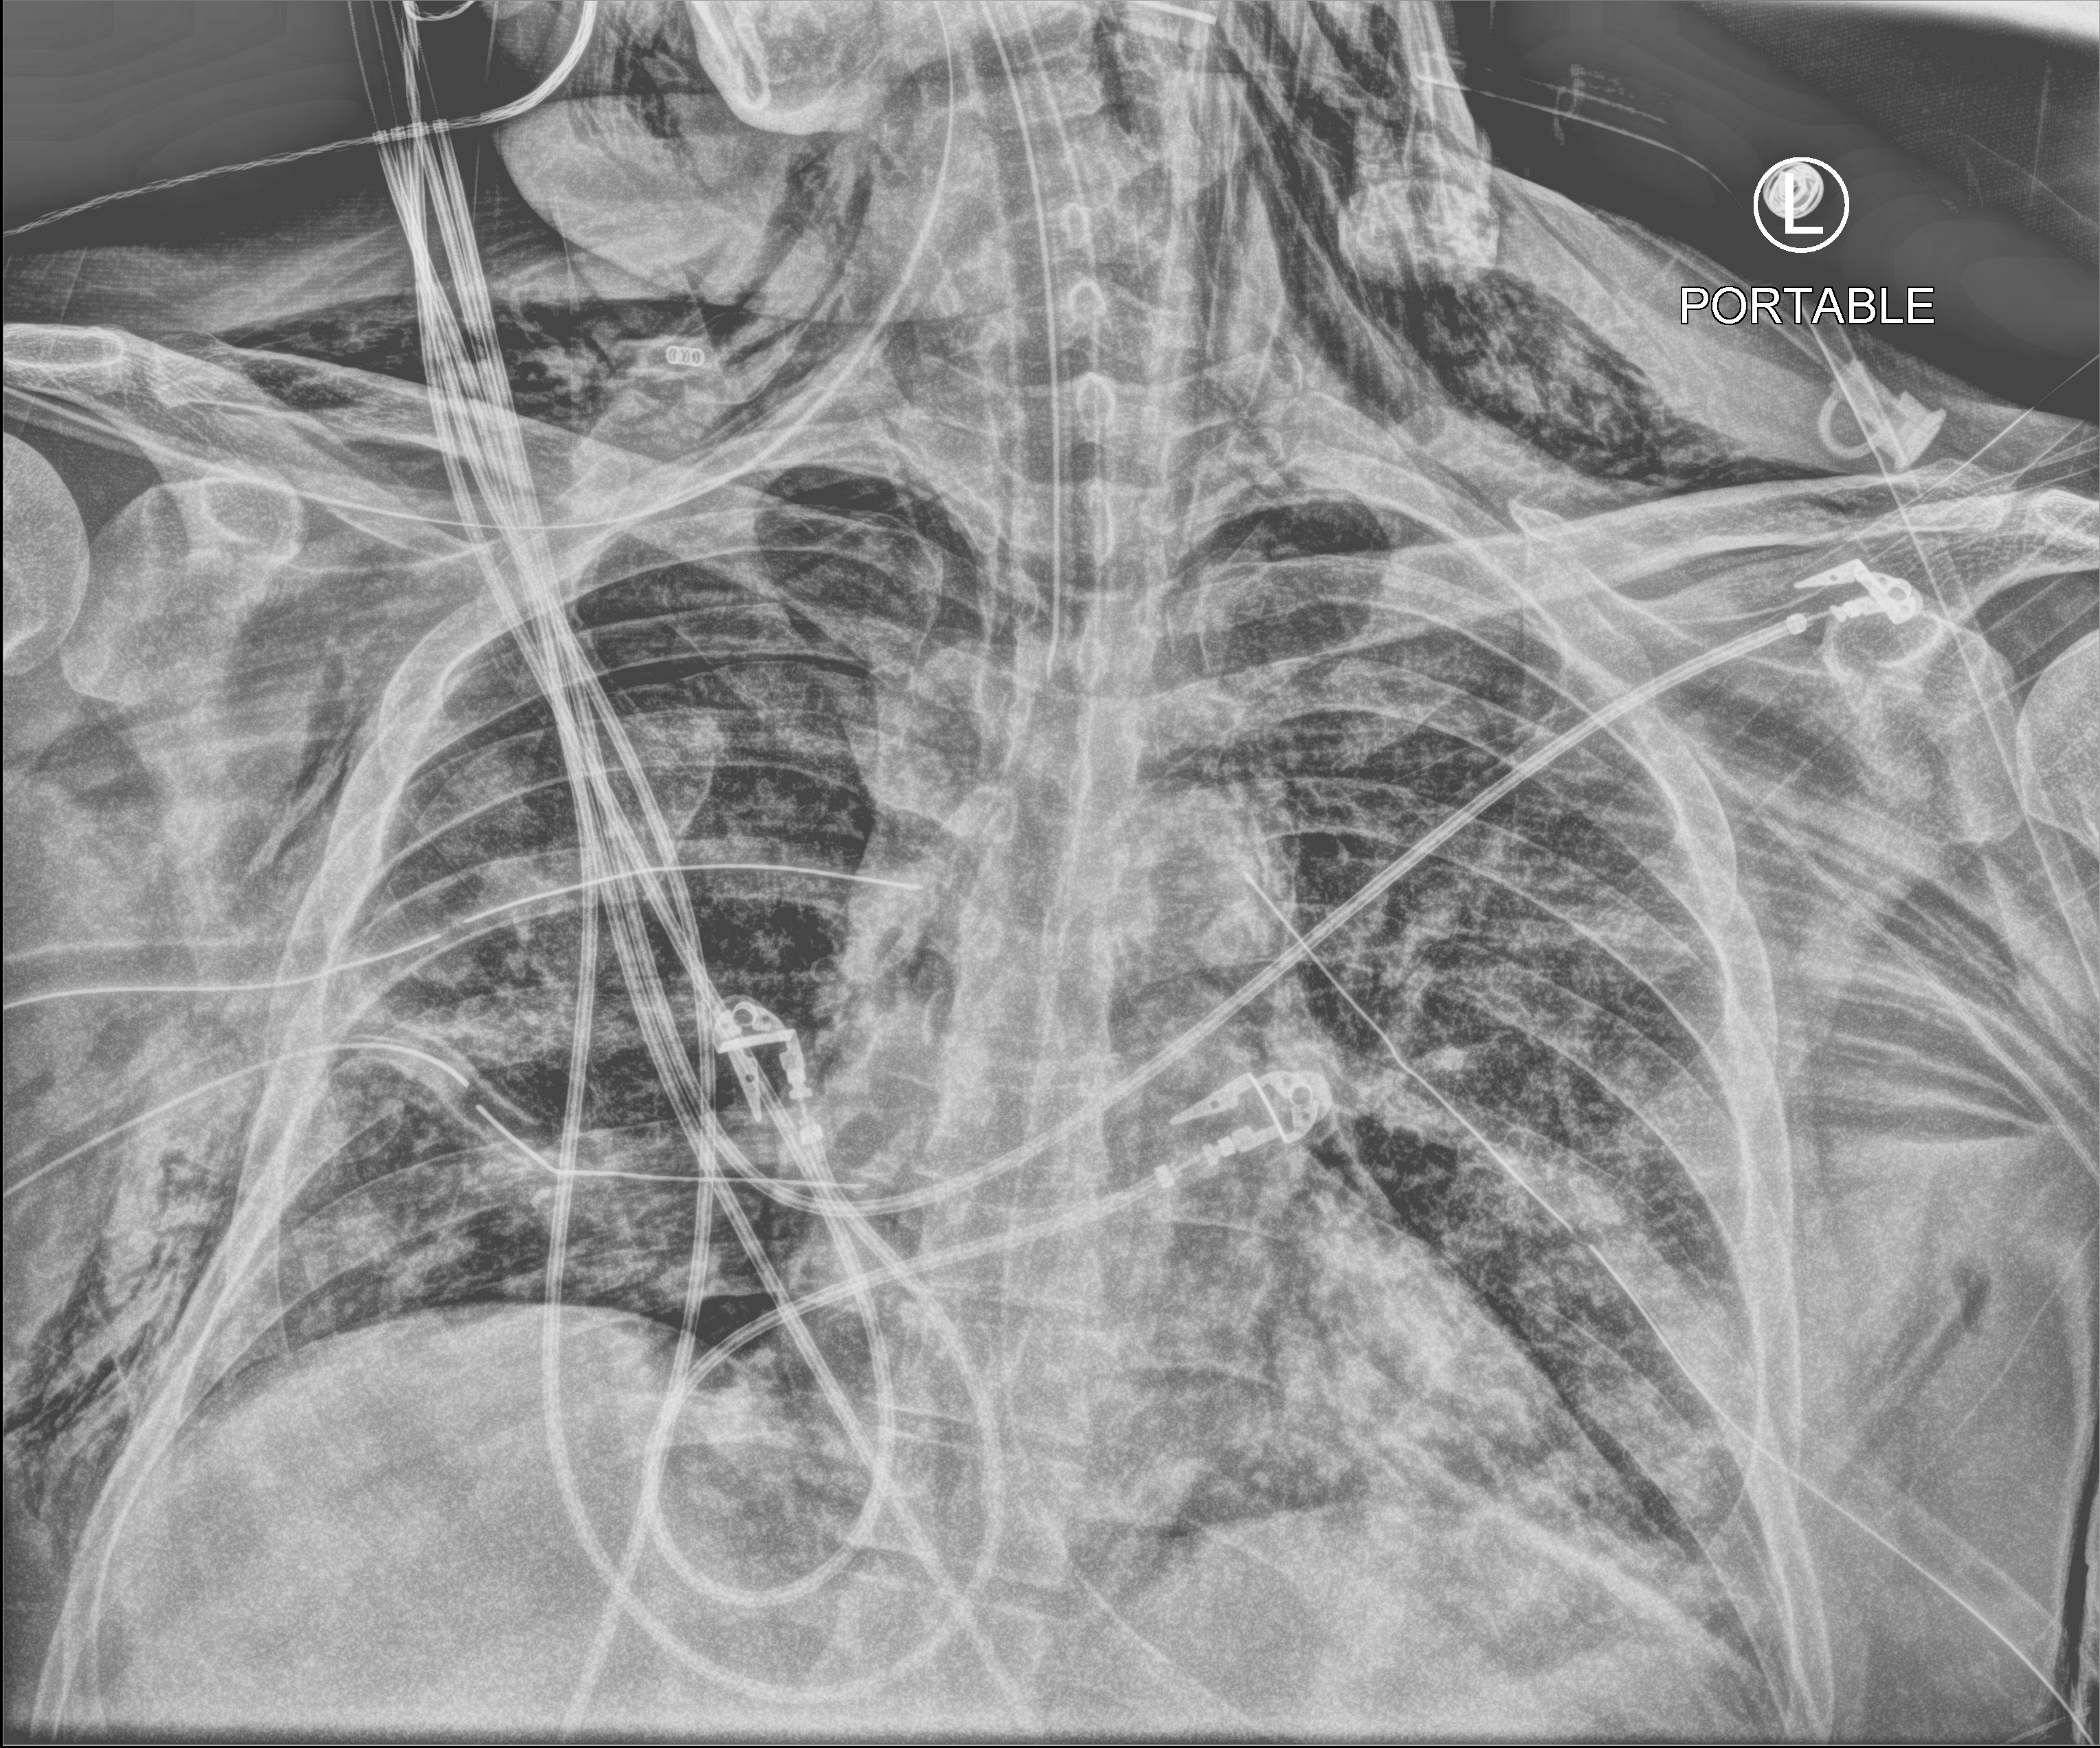
Portable chest radiograph; anteroposterior (AP) projection. Patient hospitalised with COVID-19; male, aged 18–59 years.
Admission-level facts for this patient (not findings on this image; timing relative to this image not recorded): mechanically ventilated during this hospital stay: yes.